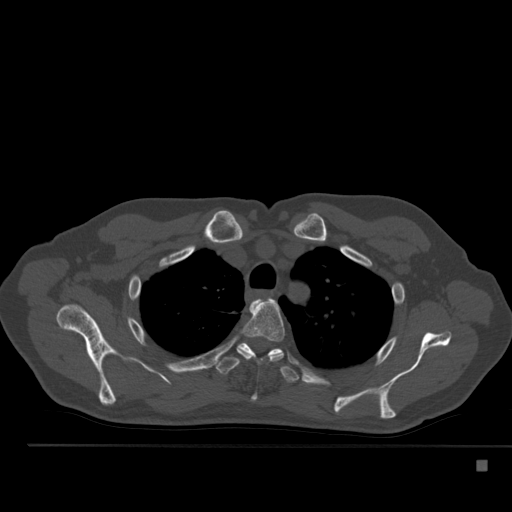
CT including the spine, one axial slice; slice 392 of 517 in the series (ordered by position); 120 kVp; bone window (W 1800 / L 400 HU); 1.5 mm slice thickness; 512 × 512 image matrix, field of view 408 × 408 mm. Male patient, age 70 years. From the clinical record (not read from this slice): primary cancer: renal.
Structures marked on this image (semi-automatically segmented with operator editing):
- T2 vertebra: bounding box [x1, y1, x2, y2] px = [254, 300, 260, 302]
- T3 vertebra: [237, 299, 285, 401]
- T4 vertebra: [216, 343, 299, 383]